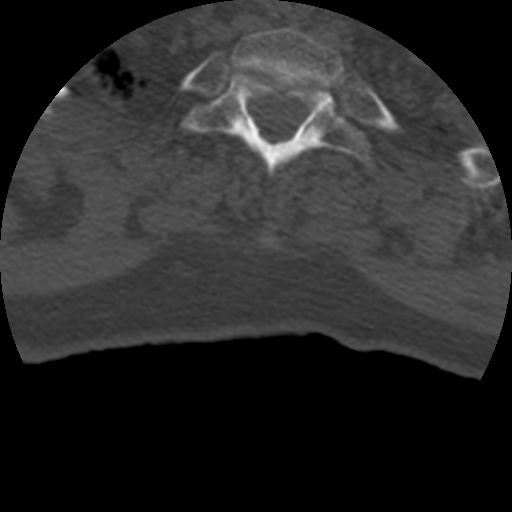
CT including the spine, one axial slice; position 372 of 399 along the scan axis; reconstruction kernel STANDARD; 120 kVp; bone window (W 1800 / L 400 HU); 512 × 512 image matrix, field of view 160 × 160 mm. Patient age 69 years. Case-level facts recorded for this patient, not image findings: primary cancer: prostate.
Outlined on this slice (semi-automatically segmented with operator editing):
- T1 vertebra: bounding box <233,28,343,94> (left, top, right, bottom; pixels)
- T2 vertebra: <186,73,374,179>